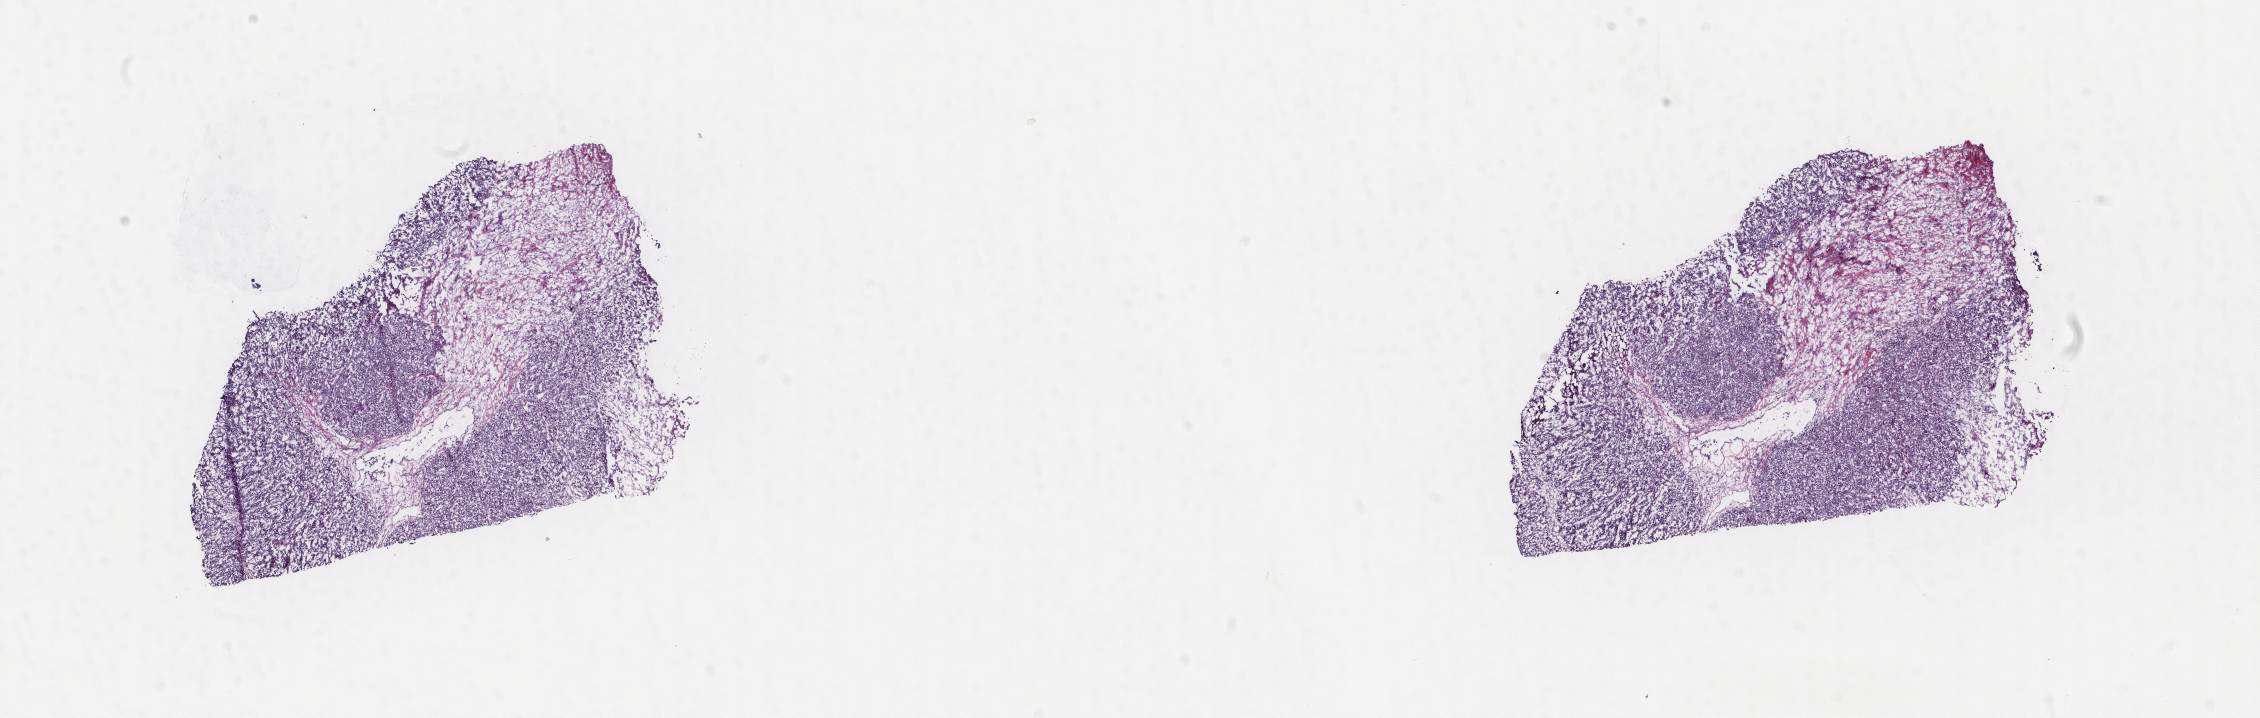
Whole-slide histology image, H&E — low-resolution overview of the scanned area, about 17.9 x 5.7 mm (acquisition: 40x scan). Frozen section from the top of the tissue portion. Metastatic tumour sample, sampled site: skin of upper limb and shoulder. Male, age 82 years at initial diagnosis. Composition of this section per pathologist review: tumour cells 80%, tumour nuclei 90%, normal cells 0%, stromal cells 20%, necrosis 0%. Infiltration values recorded for this section: lymphocyte infiltration 0%, monocyte infiltration 0%, neutrophil infiltration 0%.
• this section: metastatic tumour tissue
• patient diagnosis: Malignant melanoma, NOS